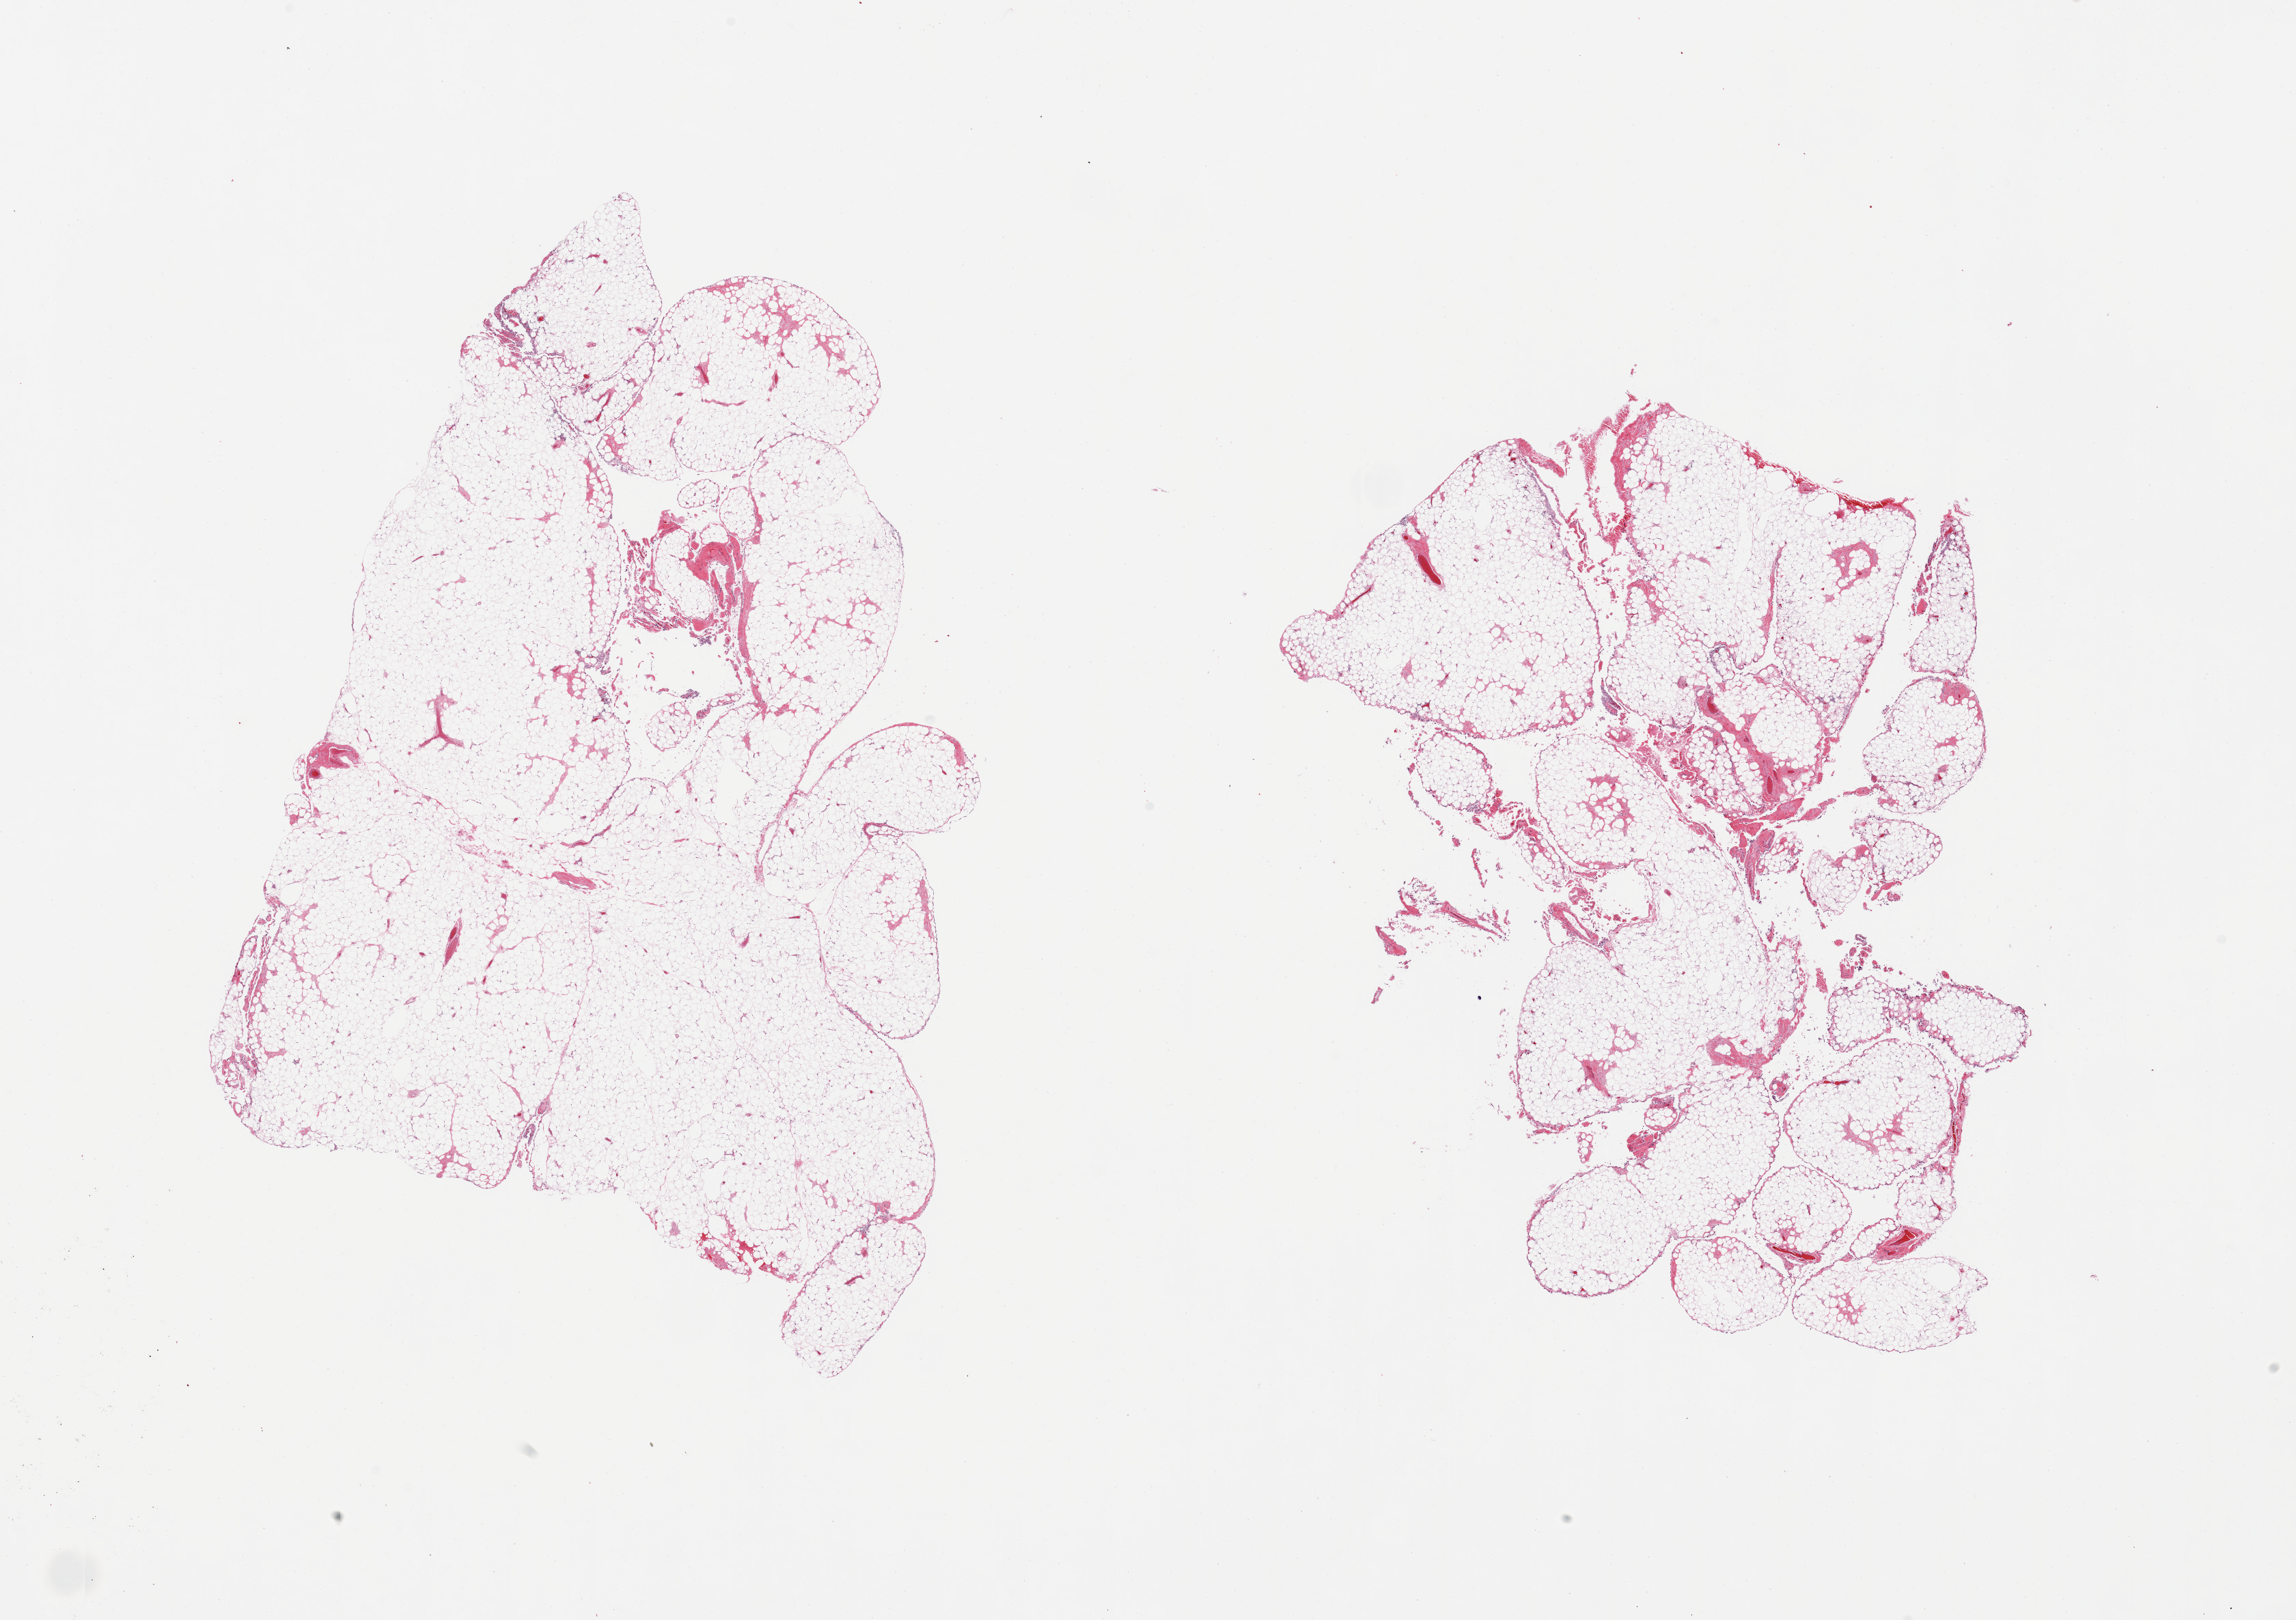
Digitized H&E-stained section, whole scanned area (about 26.6 x 18.8 mm, slide scanned at 20x) shown as a low-resolution overview, PAXgene-fixed, paraffin-embedded tissue, sampled site (target tissue): omentum, tissue donor sample. Donor: female.
Reviewer comment on this tissue sample: 2 pieces.